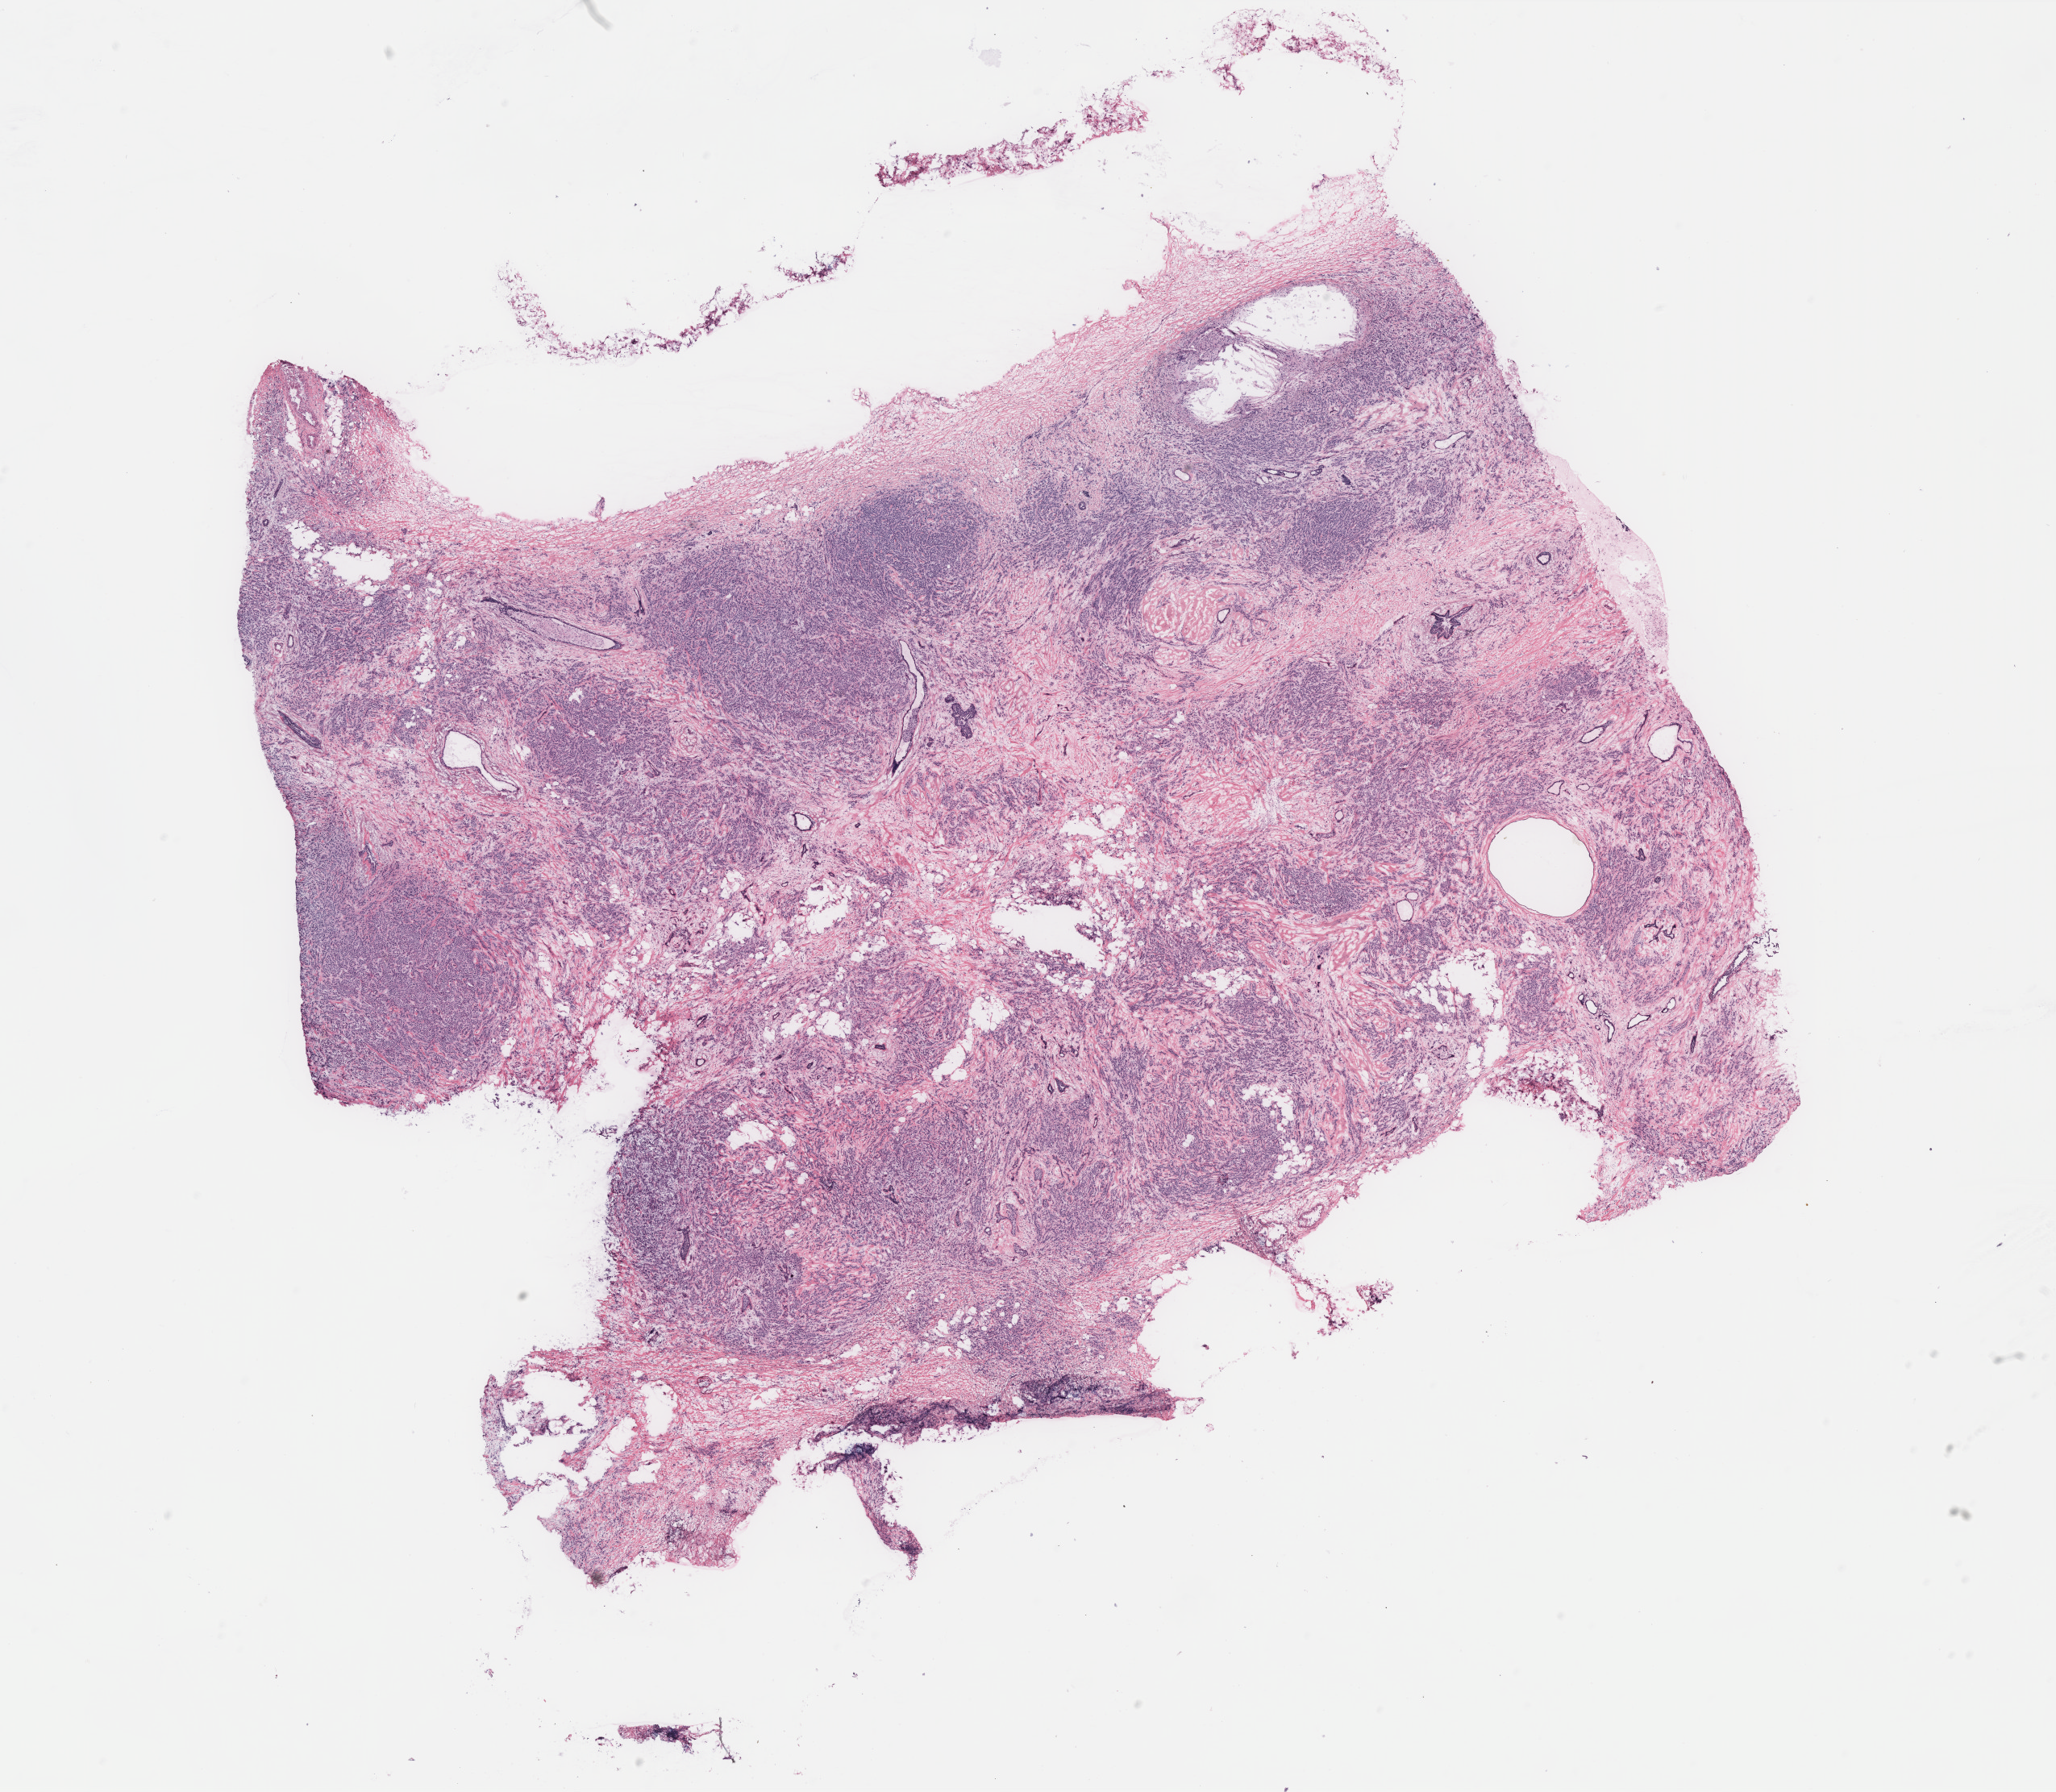
Digitized Hematoxylin and eosin (H&E) stained tissue section (whole slide), low-resolution overview of the scanned area, about 20.4 x 17.8 mm (acquisition: 40x scan); breast, tumour tissue. 79-year-old female patient.
Diagnosis: Infiltrating duct carcinoma, NOS. AJCC pathologic stage: IIIA.